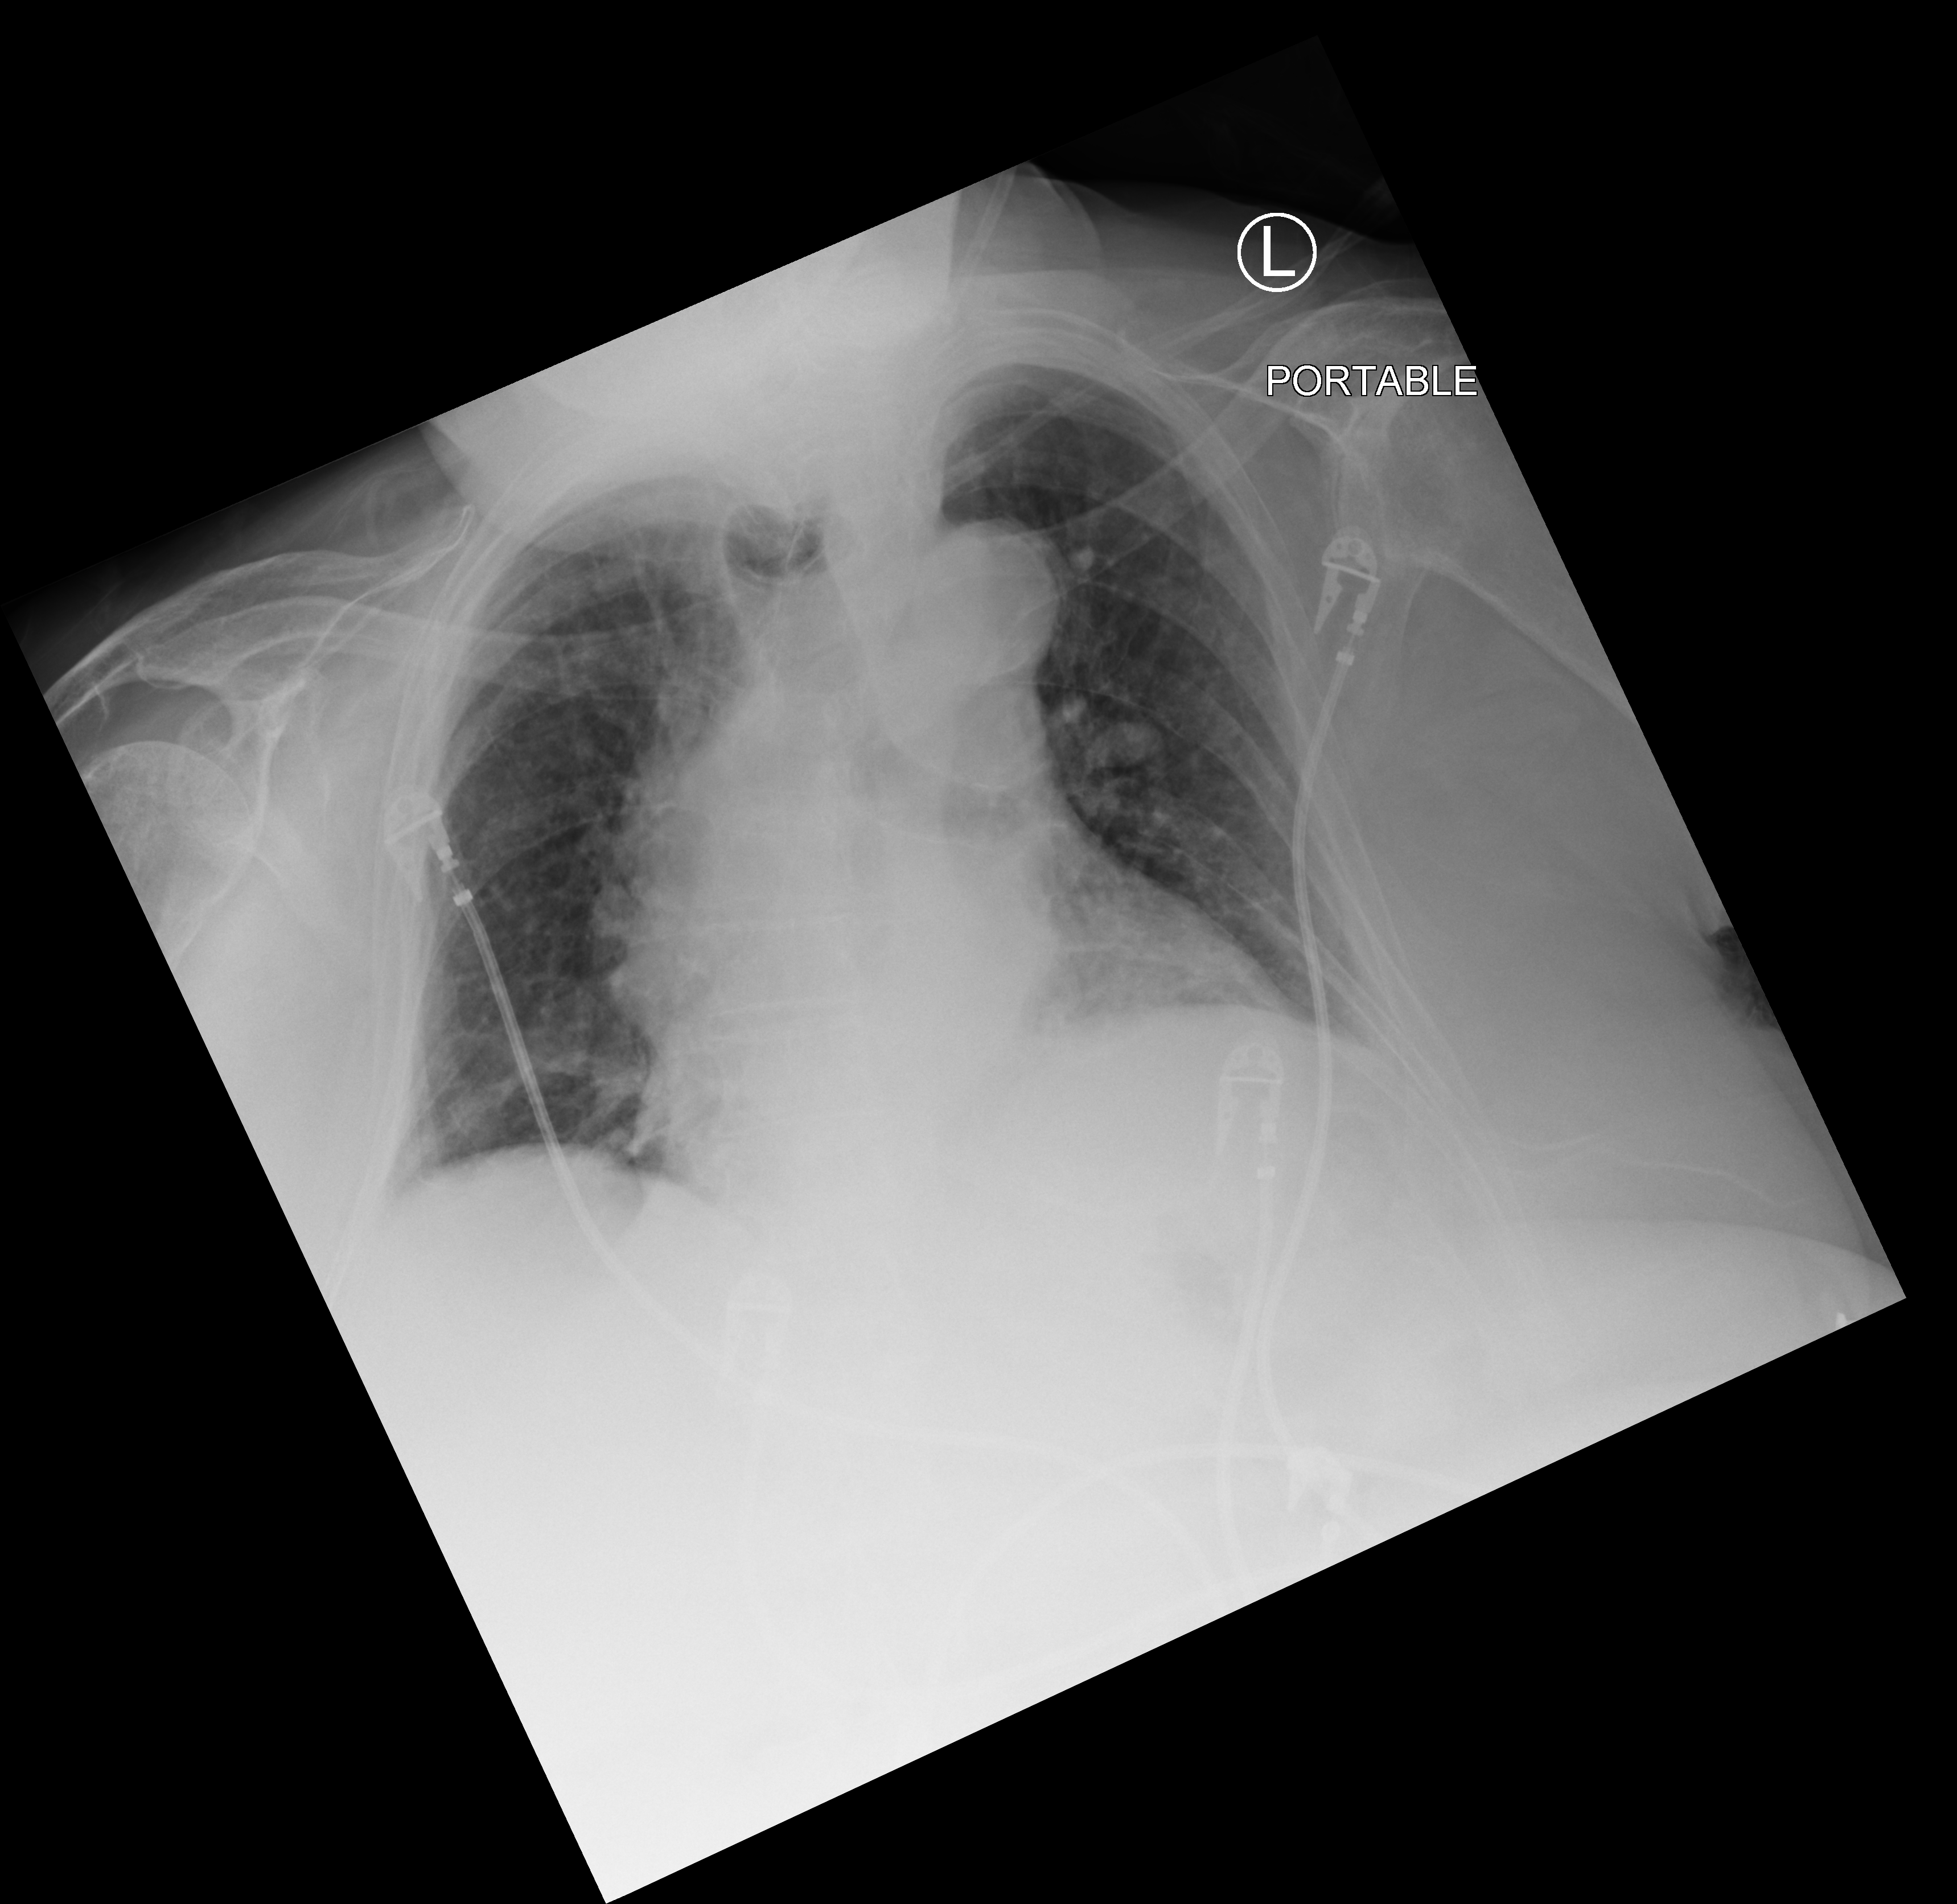
Chest X-ray (portable); anteroposterior (AP) projection. Female patient hospitalised with COVID-19, age 75–90 years.
Hospital-stay facts (about this admission, not read from this image; timing relative to this image not recorded): mechanically ventilated during this hospital stay: no.